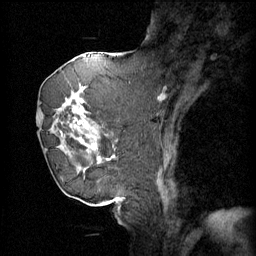
Breast MRI (dynamic contrast-enhanced), one sagittal slice; position 23 of 60 along the scan axis; 4 images stored at this slice position (order not interpretable as contrast timing); 1.5 T; TE 4.2 ms, TR 11 ms; 256 × 256 image matrix, field of view 220 × 220 mm. Female patient, age 72 years.
Annotated regions visible in this slice (semi-automatically segmented with operator editing):
- analysis volume of interest (the breast-tissue region the enhancement analysis was run in; not a lesion): bounding box (x1, y1, x2, y2) in pixels: (44, 68, 109, 163)
- tumour enhancement mask (voxels above the 70 % enhancement threshold inside the analysis volume of interest): (44, 72, 109, 161)